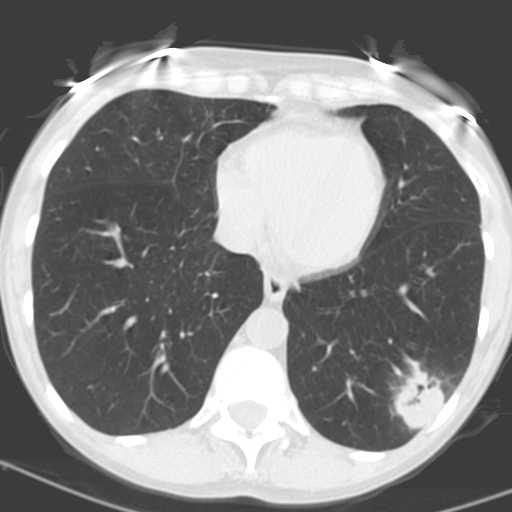
Low-dose screening chest CT, one axial slice. Position 53 of 156 along the scan axis. 120 kVp. Lung window (W 1500 / L -600 HU). 3.2 mm slice thickness. 512 × 512 image matrix.
Outlined on this slice (expert manual segmentation):
- lesion 1 (tumor, lower lobe of left lung): bounding box <393,360,446,430> (left, top, right, bottom; pixels)